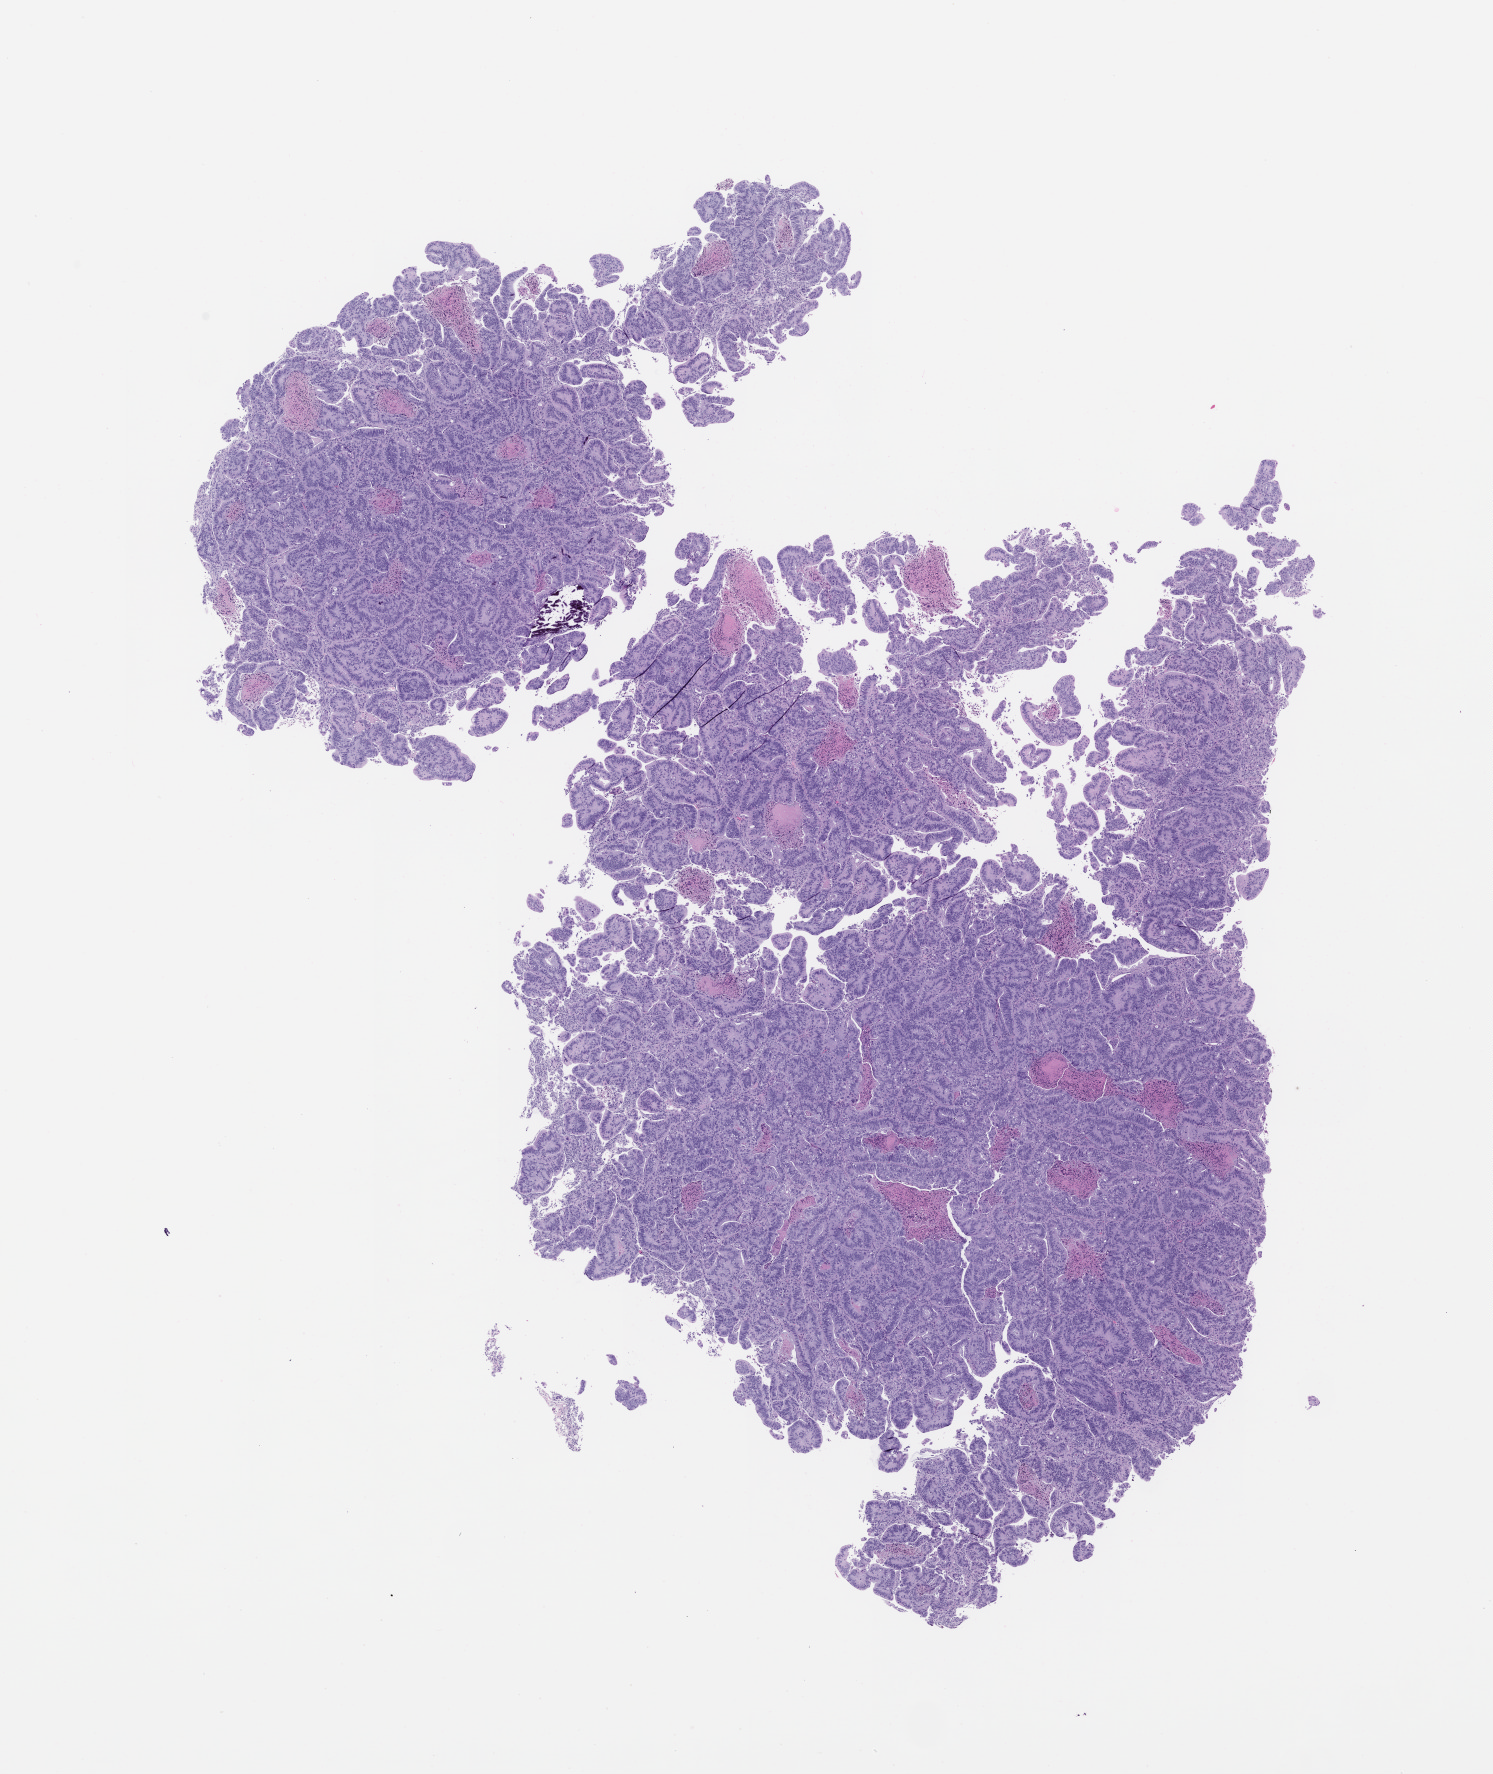
Whole-slide image, haematoxylin and eosin: patient-derived xenograft (human tumor grown in a mouse), passage 1 — a low-resolution overview of the entire scanned area, about 12.0 x 14.2 mm, formalin-fixed, paraffin-embedded (FFPE) tissue, tumor site category: colon.
Originating patient diagnosis: Colon Adenocarcinoma.